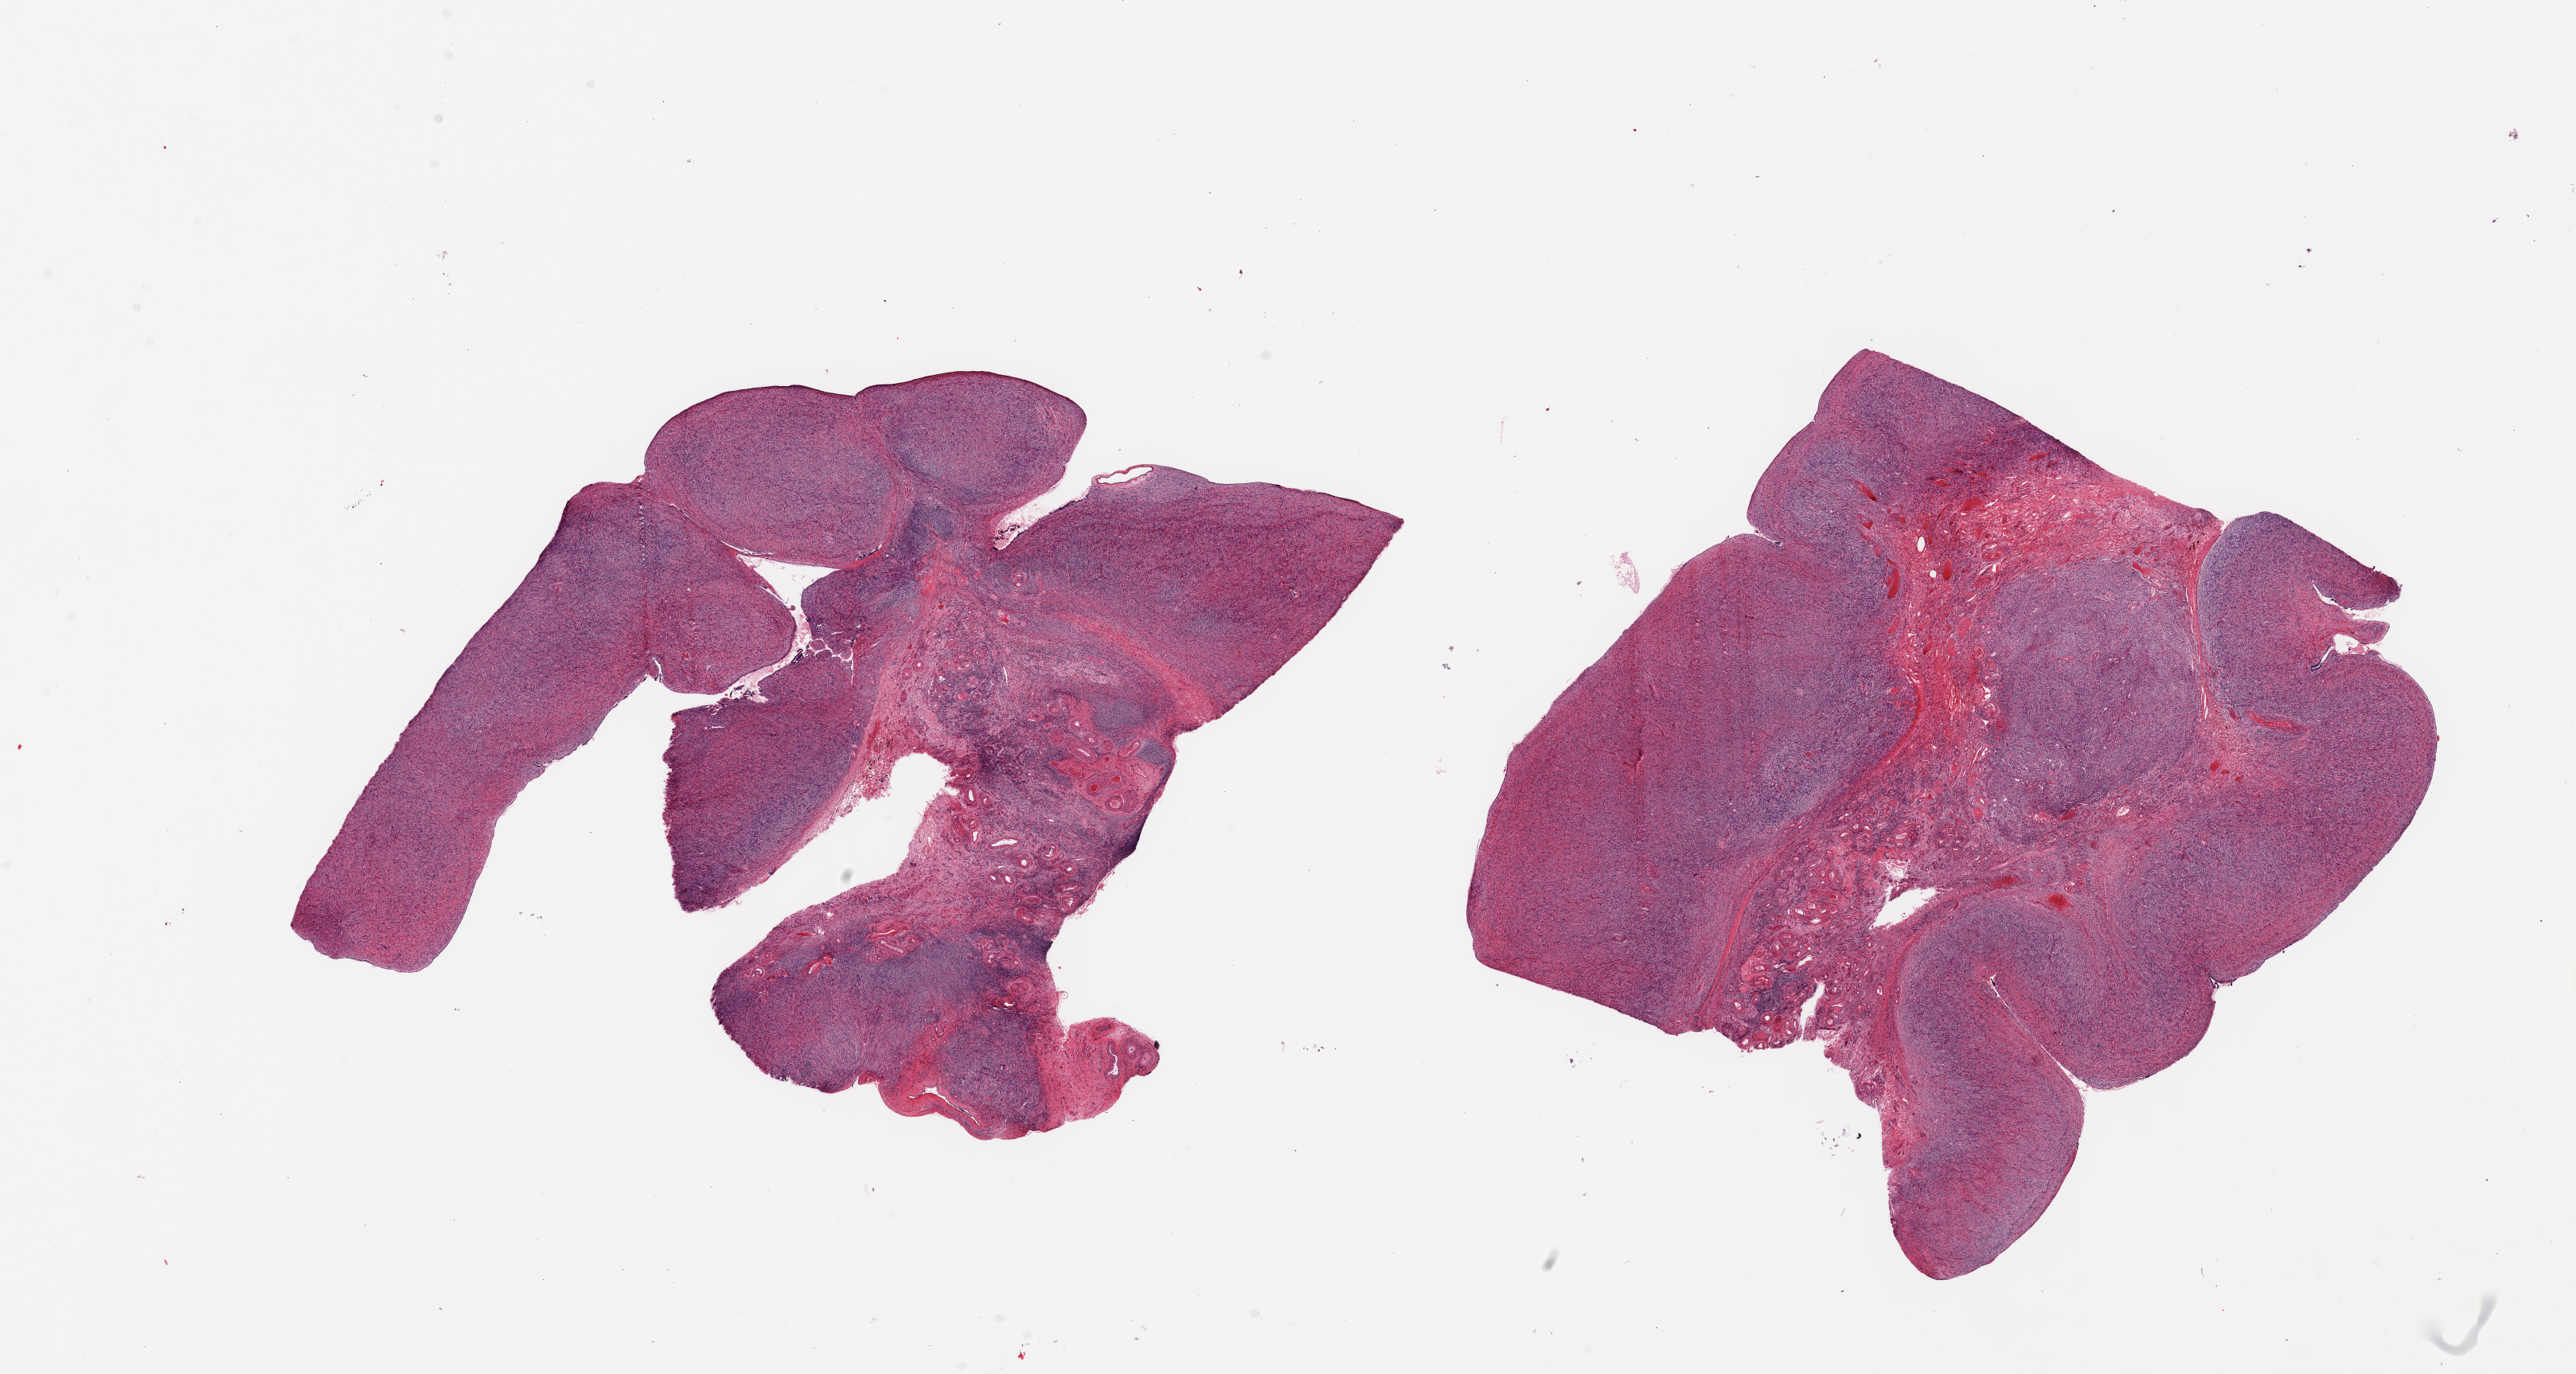
Digitized haematoxylin and eosin-stained section, whole scanned area (about 25.6 x 13.7 mm) shown as a low-resolution overview; PAXgene-fixed paraffin-embedded (PFPE) section; sampled site (target tissue): ovary; tissue donor sample. Donor sex: female.
Review note (as recorded): 2 pieces; small corpora albicantia.